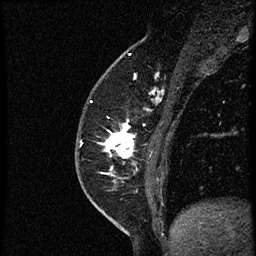
Breast MRI (dynamic contrast-enhanced), one sagittal slice; slice 21 of 56 in the series (ordered by position); dynamic contrast-enhanced study with each time point stored as its own series, time point 2 of 4 at this slice position (early post-contrast, ordered by acquisition time); 1.5 T; TE 4.2 ms, TR 18.9 ms; 256 × 256 image matrix, field of view 200 × 200 mm. Female patient. Case-level facts recorded for this patient, not image findings: setting: breast cancer imaged before/during neoadjuvant chemotherapy; receptor status: HER2-positive.
Structures marked on this image (semi-automatically segmented with operator editing):
- analysis volume of interest (the breast-tissue region the enhancement analysis was run in; not a lesion): bounding box (x1, y1, x2, y2) in pixels: (97, 86, 174, 189)
- tumour enhancement mask (voxels above the 100 % enhancement threshold inside the analysis volume of interest): (105, 120, 136, 174)